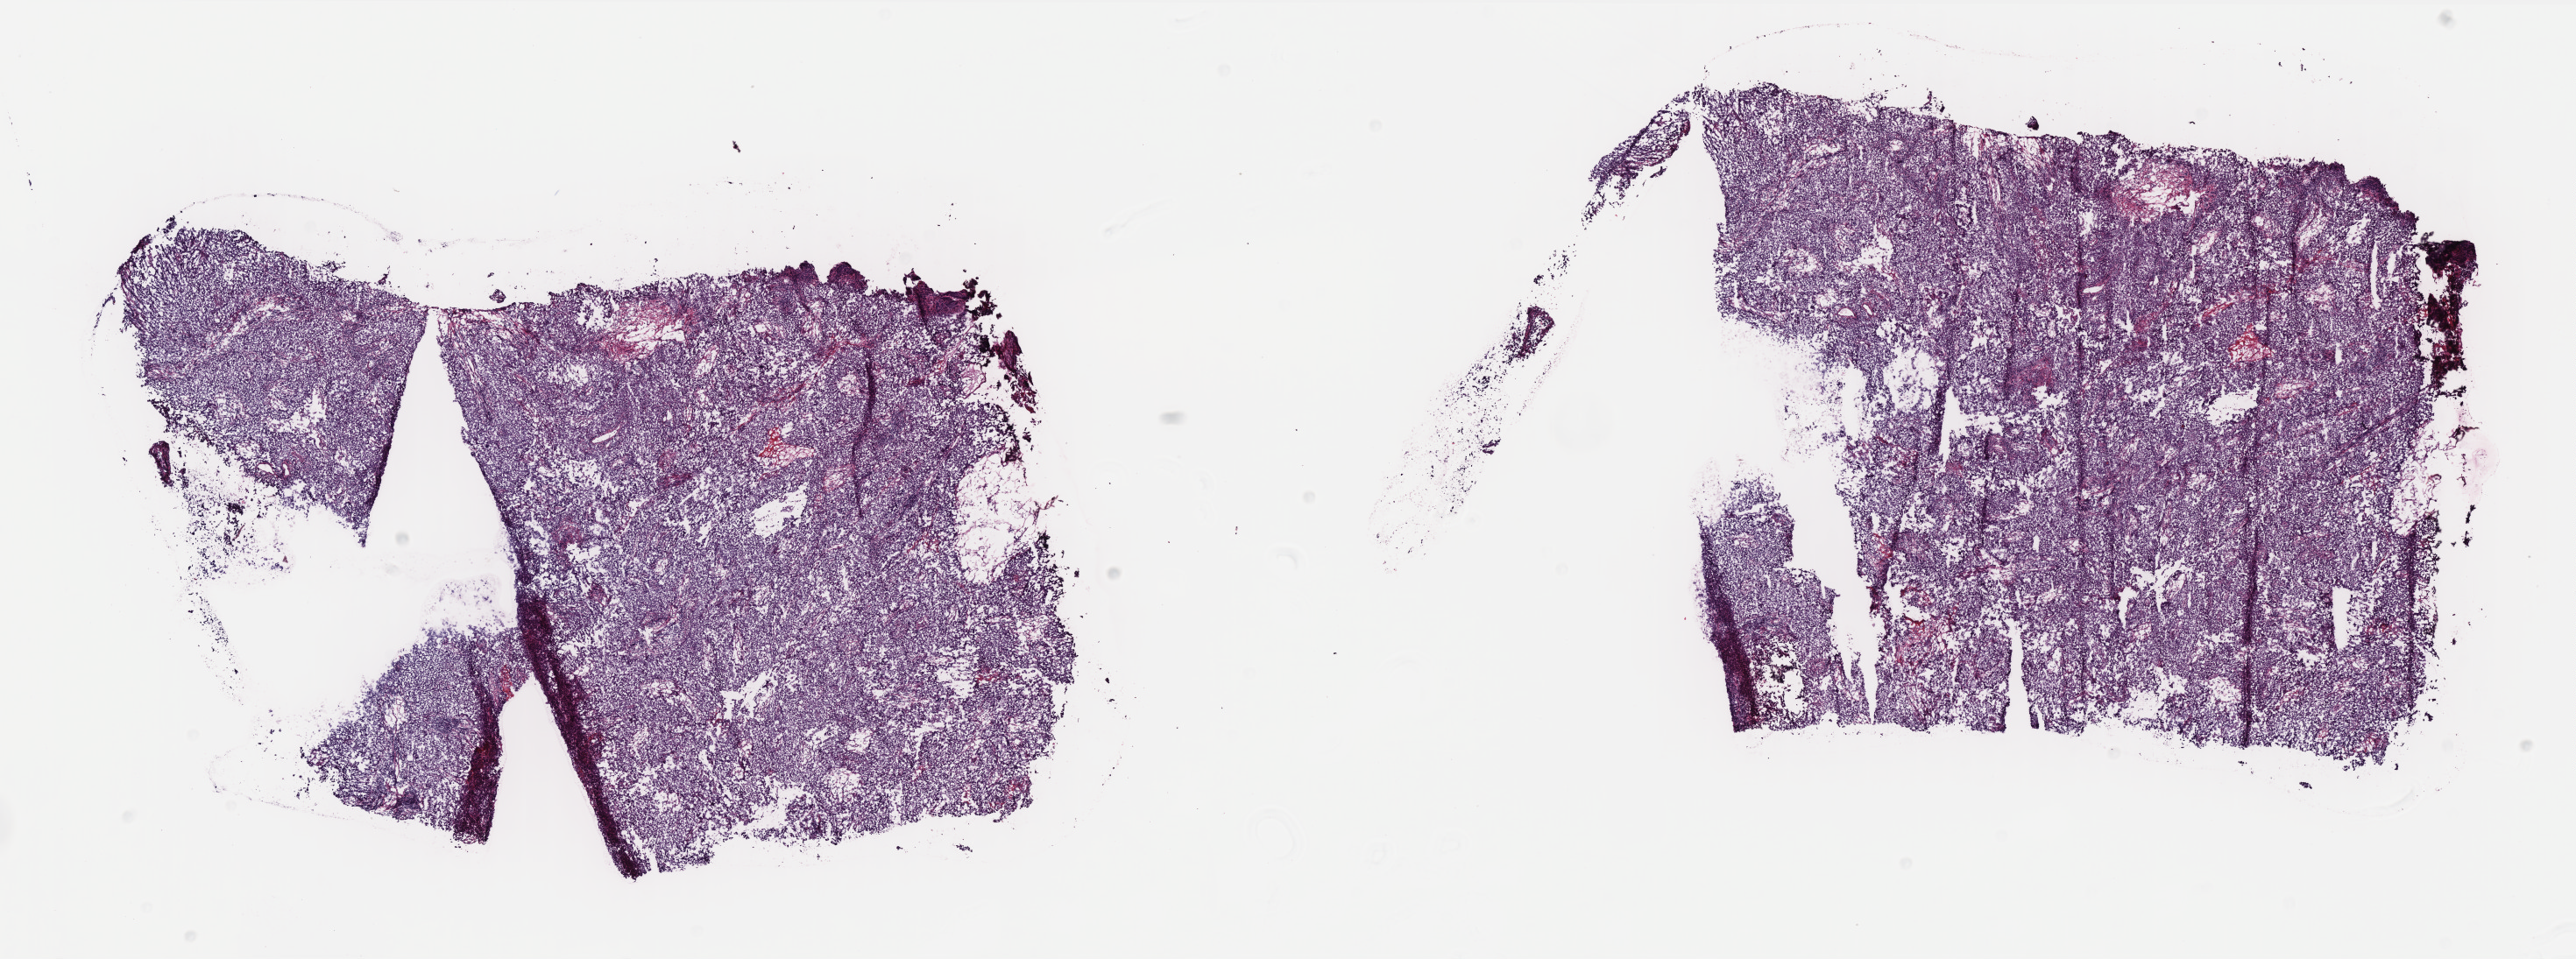
Whole-slide histology image, H&E-stained, whole scanned area (about 23.6 x 8.8 mm, from a 40x scan) shown as a low-resolution overview. Frozen section. Primary tumour sample from the uterus. Female, age 73 years at initial diagnosis. Histologic grade: G3 (poorly differentiated). Pathologist review of this section (percent, as recorded): tumour cells 95%, tumour nuclei 80%, normal cells 0%, stromal cells 0%, necrosis 5%. Inflammatory infiltration, as recorded: lymphocyte infiltration 15%, monocyte infiltration 3%, neutrophil infiltration 0%.
• lymph nodes positive (case pathology): 0 of 21 examined
• diagnosis: Clear cell adenocarcinoma, NOS (endometrium)
• FIGO stage: IB